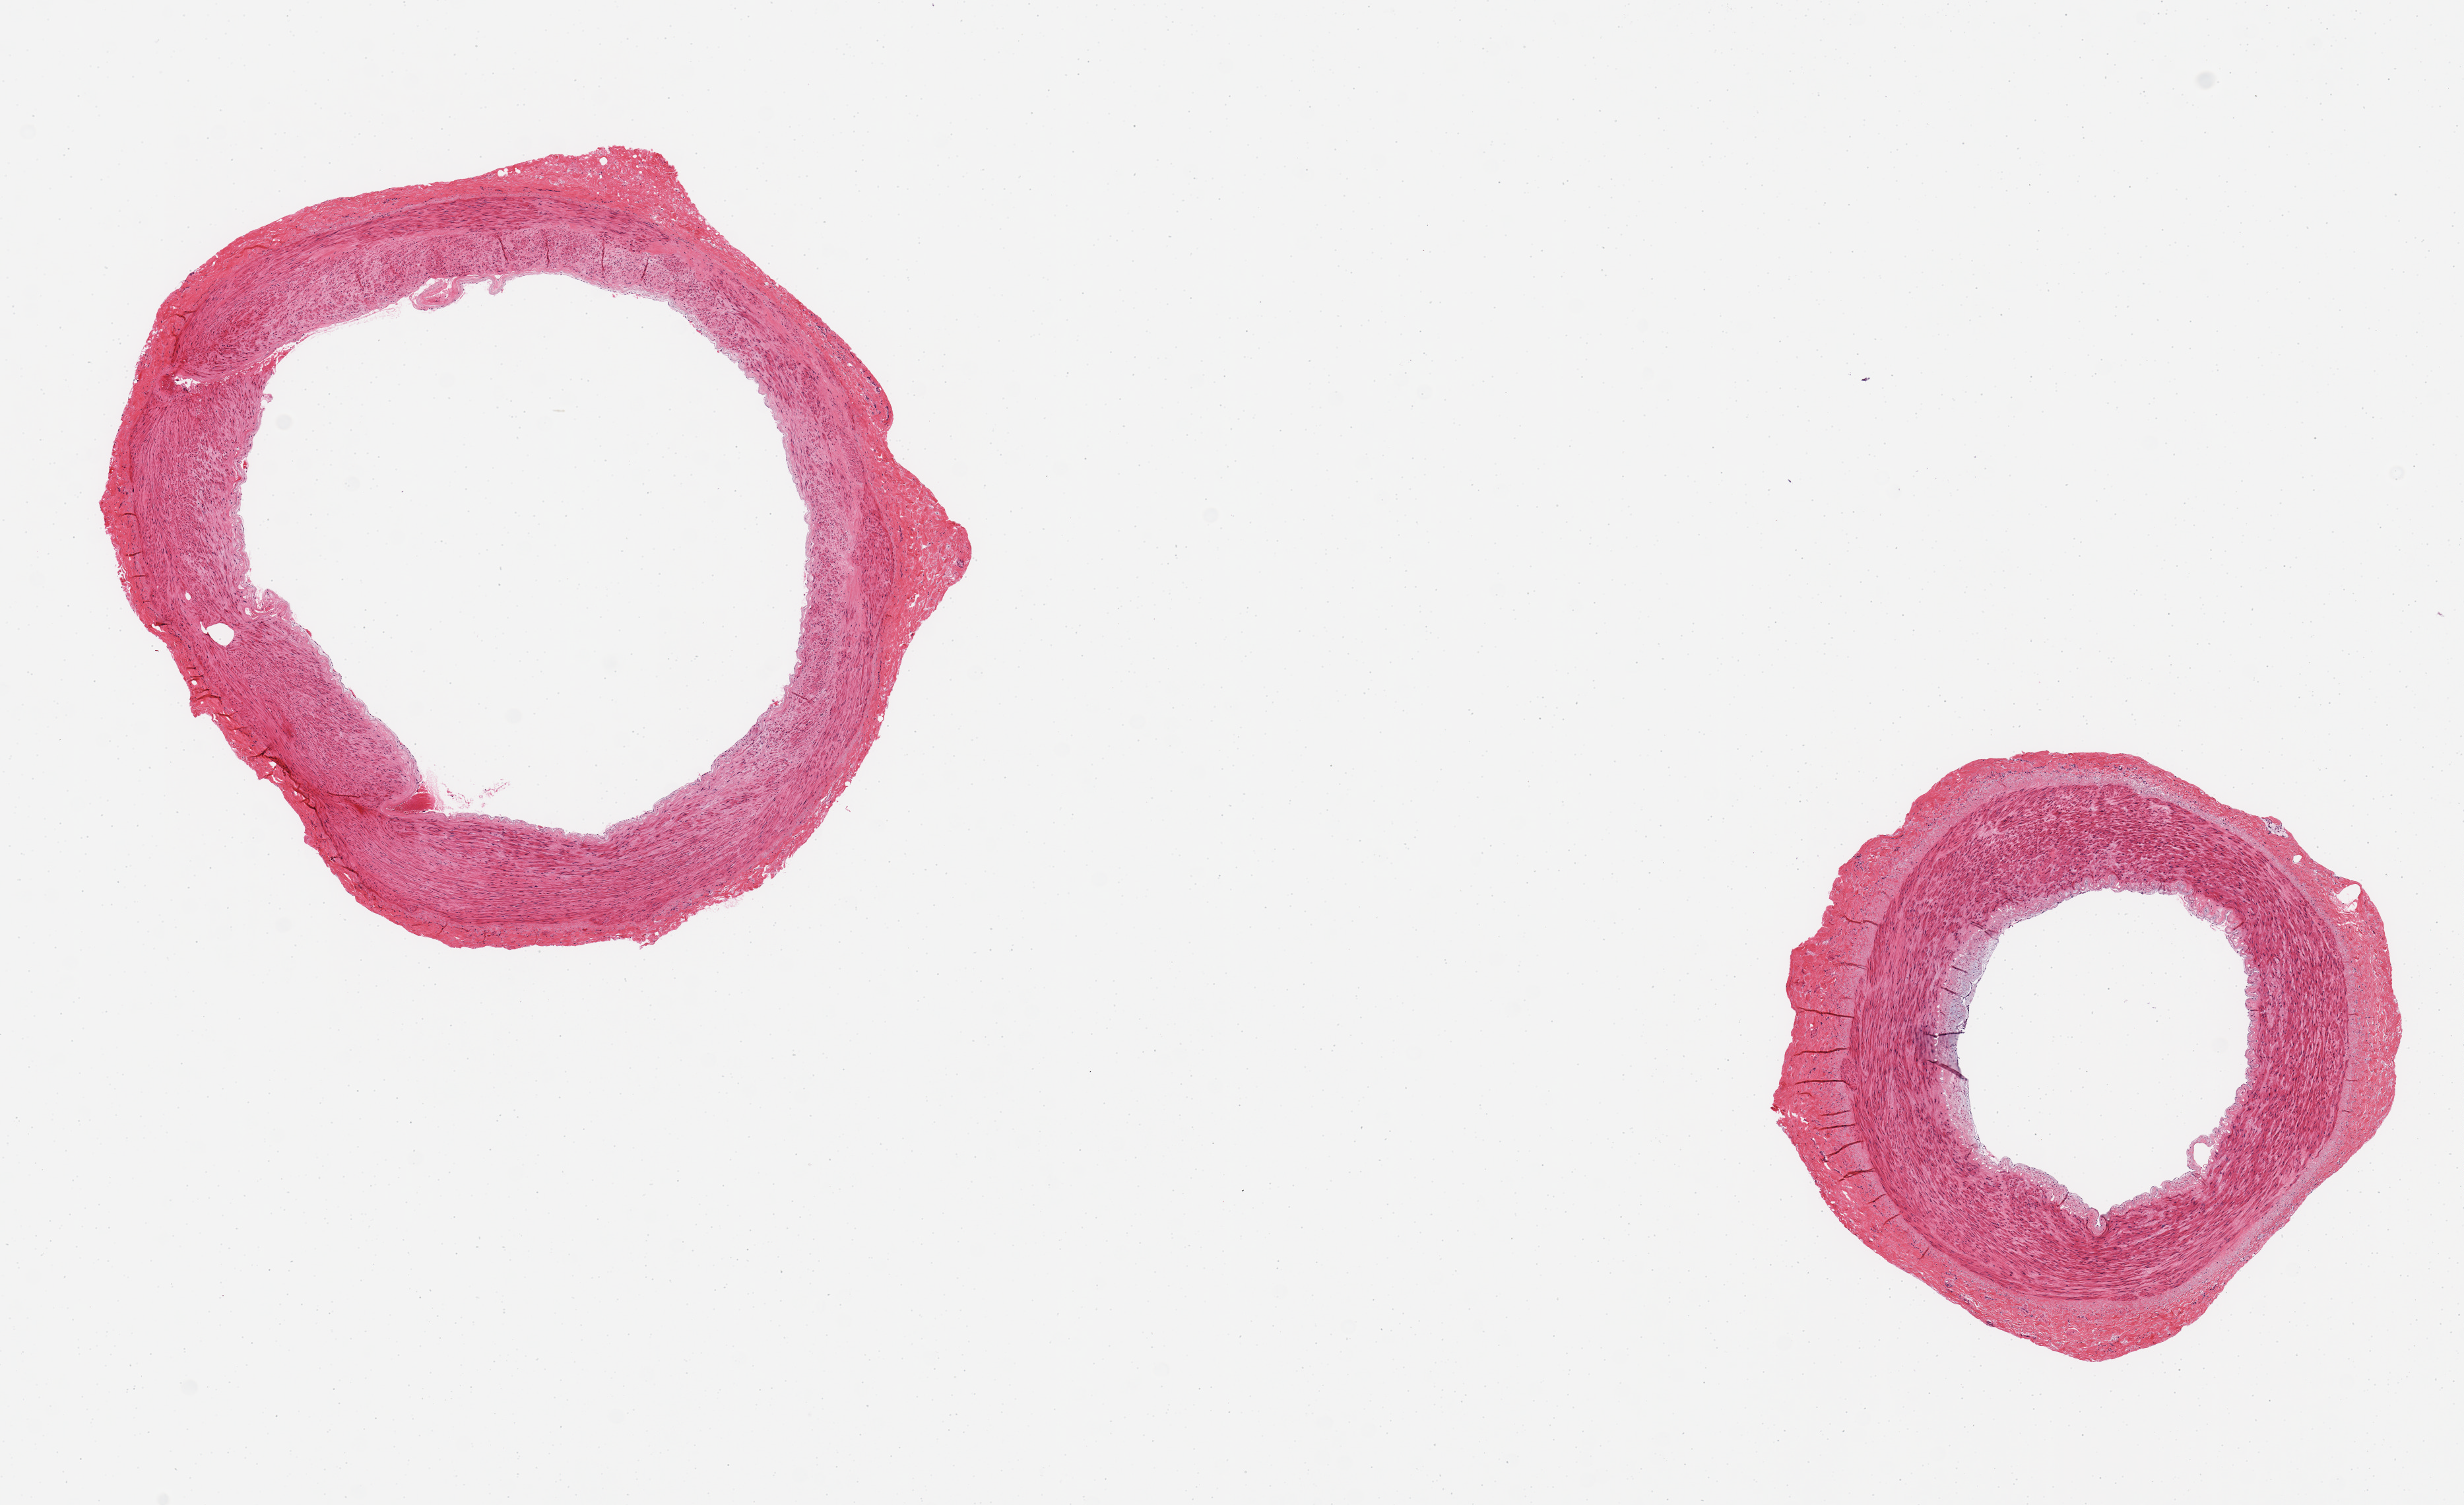
Digitized hematoxylin and eosin (H&E)-stained section — shown as a low-resolution overview of the whole scanned area (about 14.8 x 9.0 mm). PAXgene-fixed paraffin-embedded (PFPE) section. Sampled site (target tissue): tibial artery. Donor tissue sample. Donor sex: female.
Reviewer comment on this tissue sample: 2 pieces, some intimal thickening.